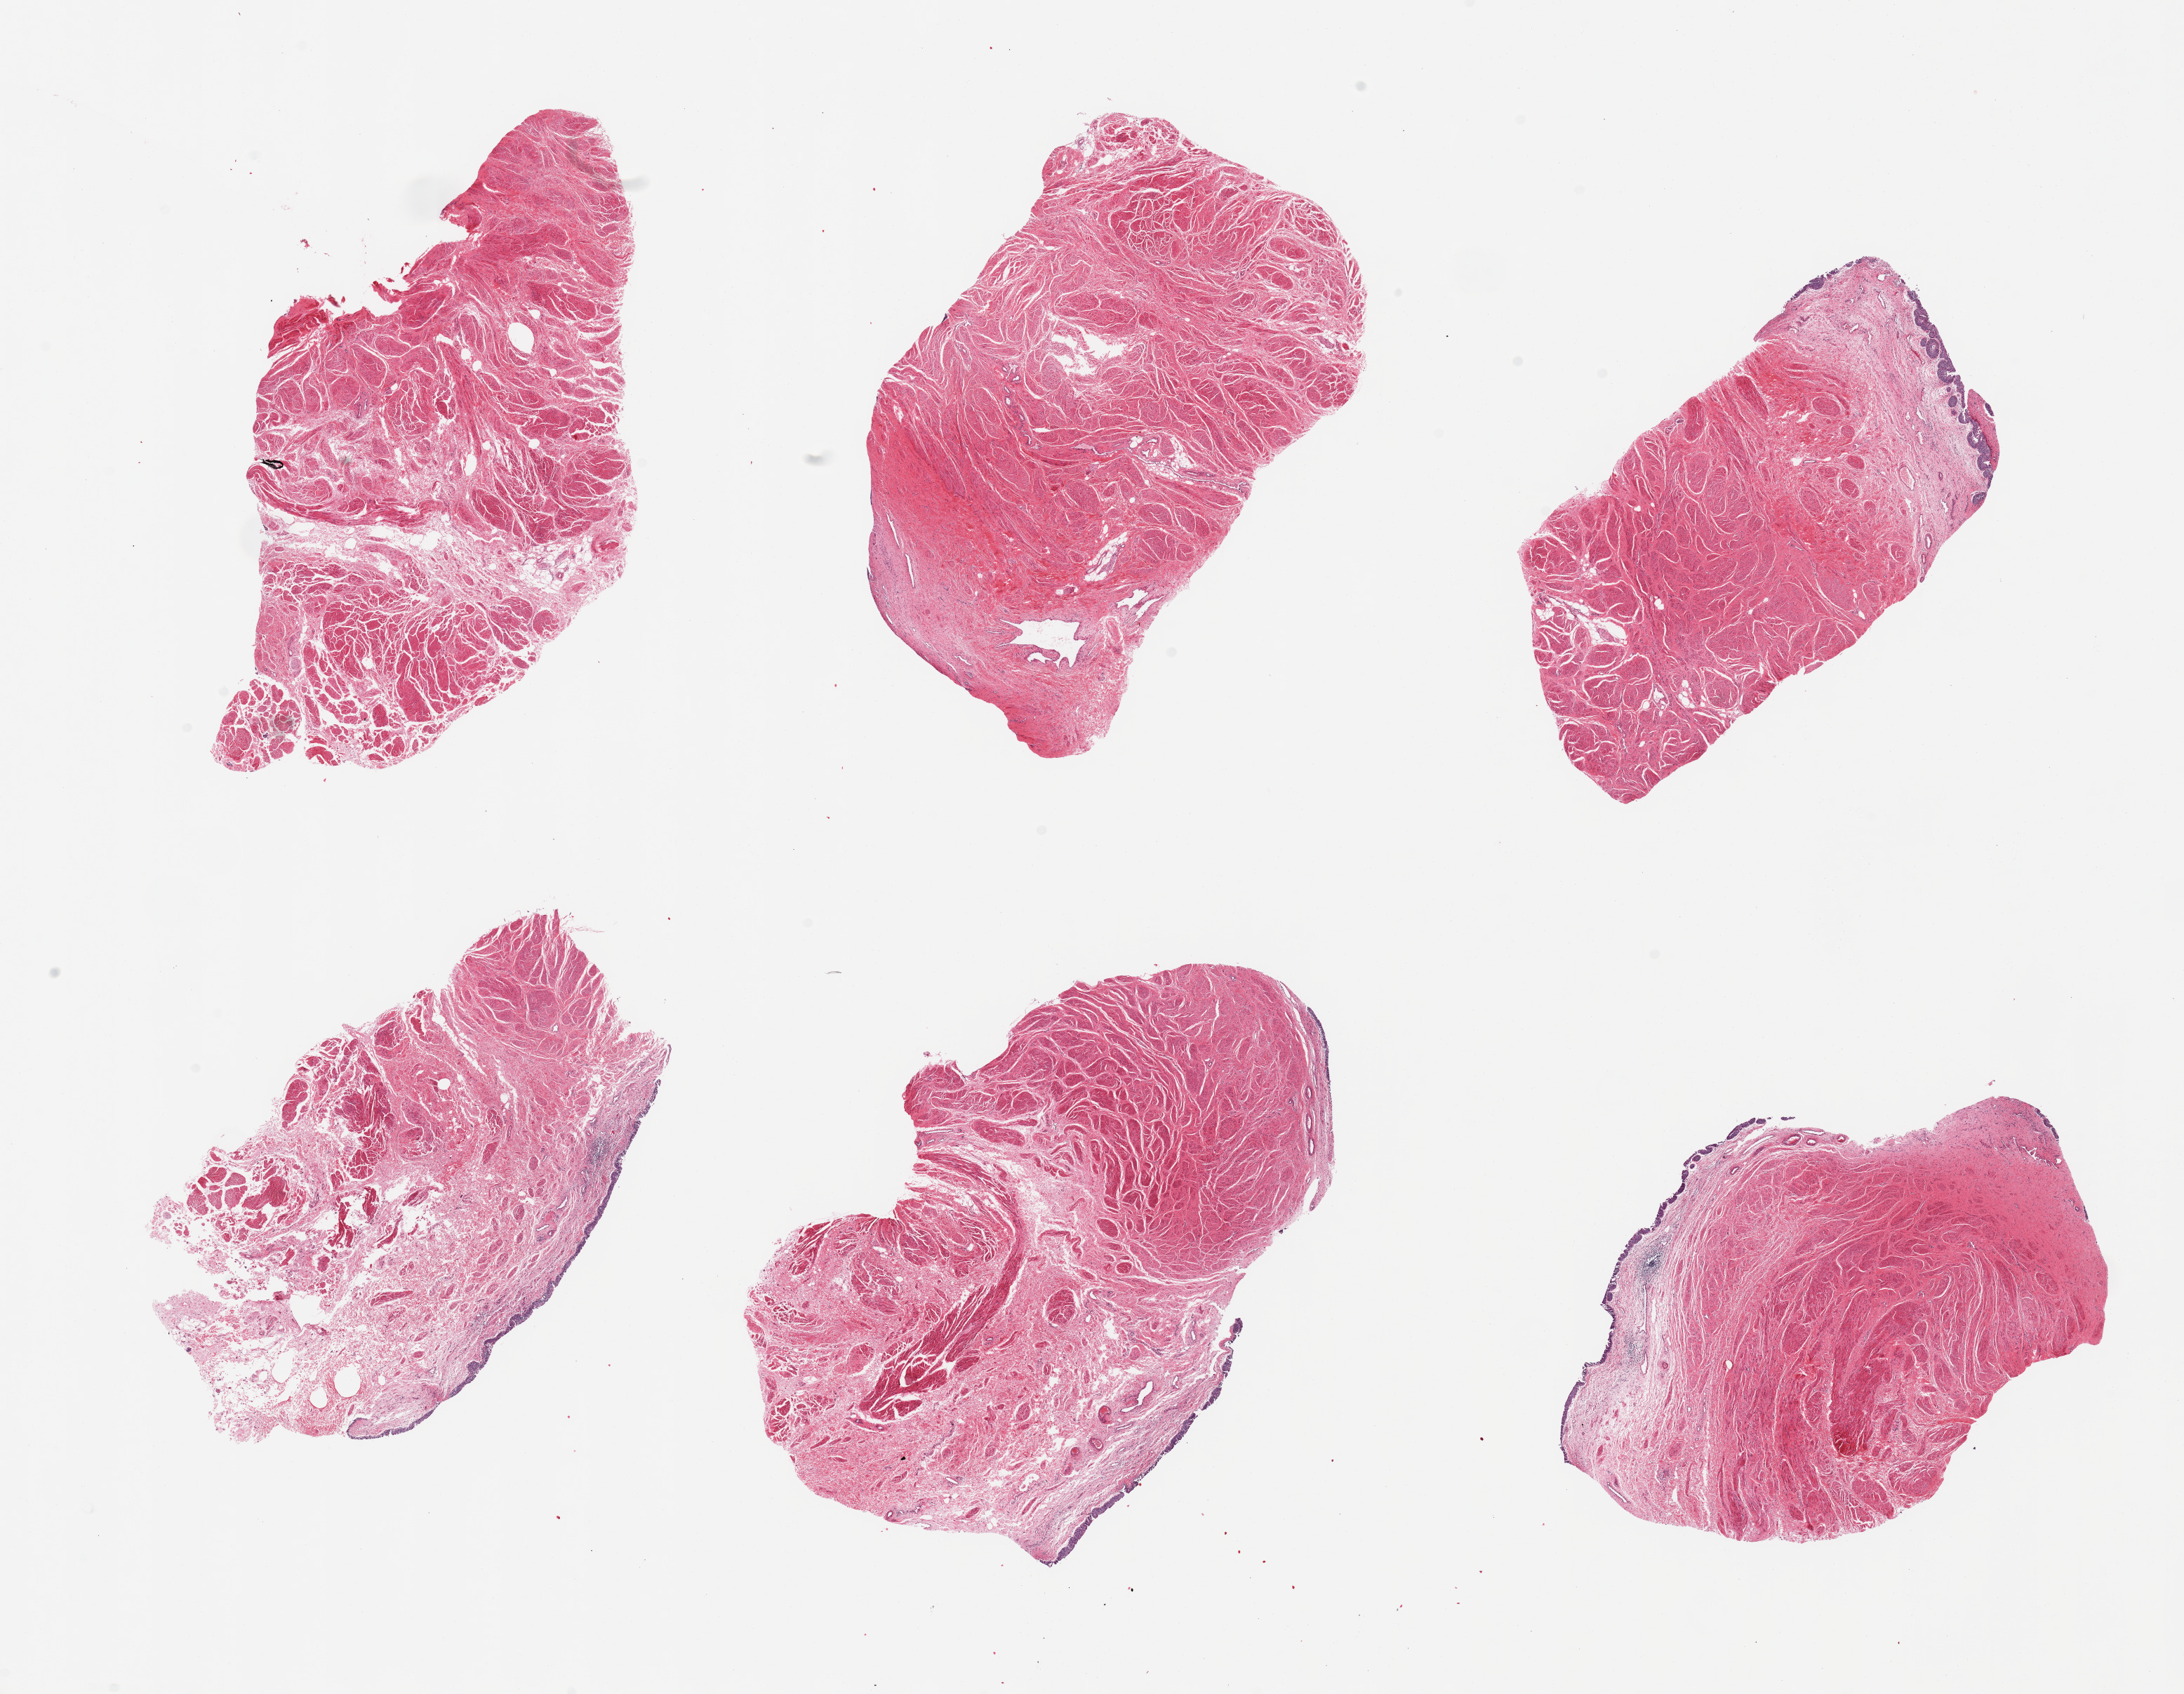
Hematoxylin and eosin (H&E) whole-slide image, low-resolution overview of the scanned area, about 24.6 x 19.1 mm. PAXgene-fixed paraffin-embedded (PFPE) section. Target tissue: vagina. Donor tissue sample. Donor: female.
Pathologist's review note for this sample: 6 pieces; partly atrophic, sloughed epithelium.